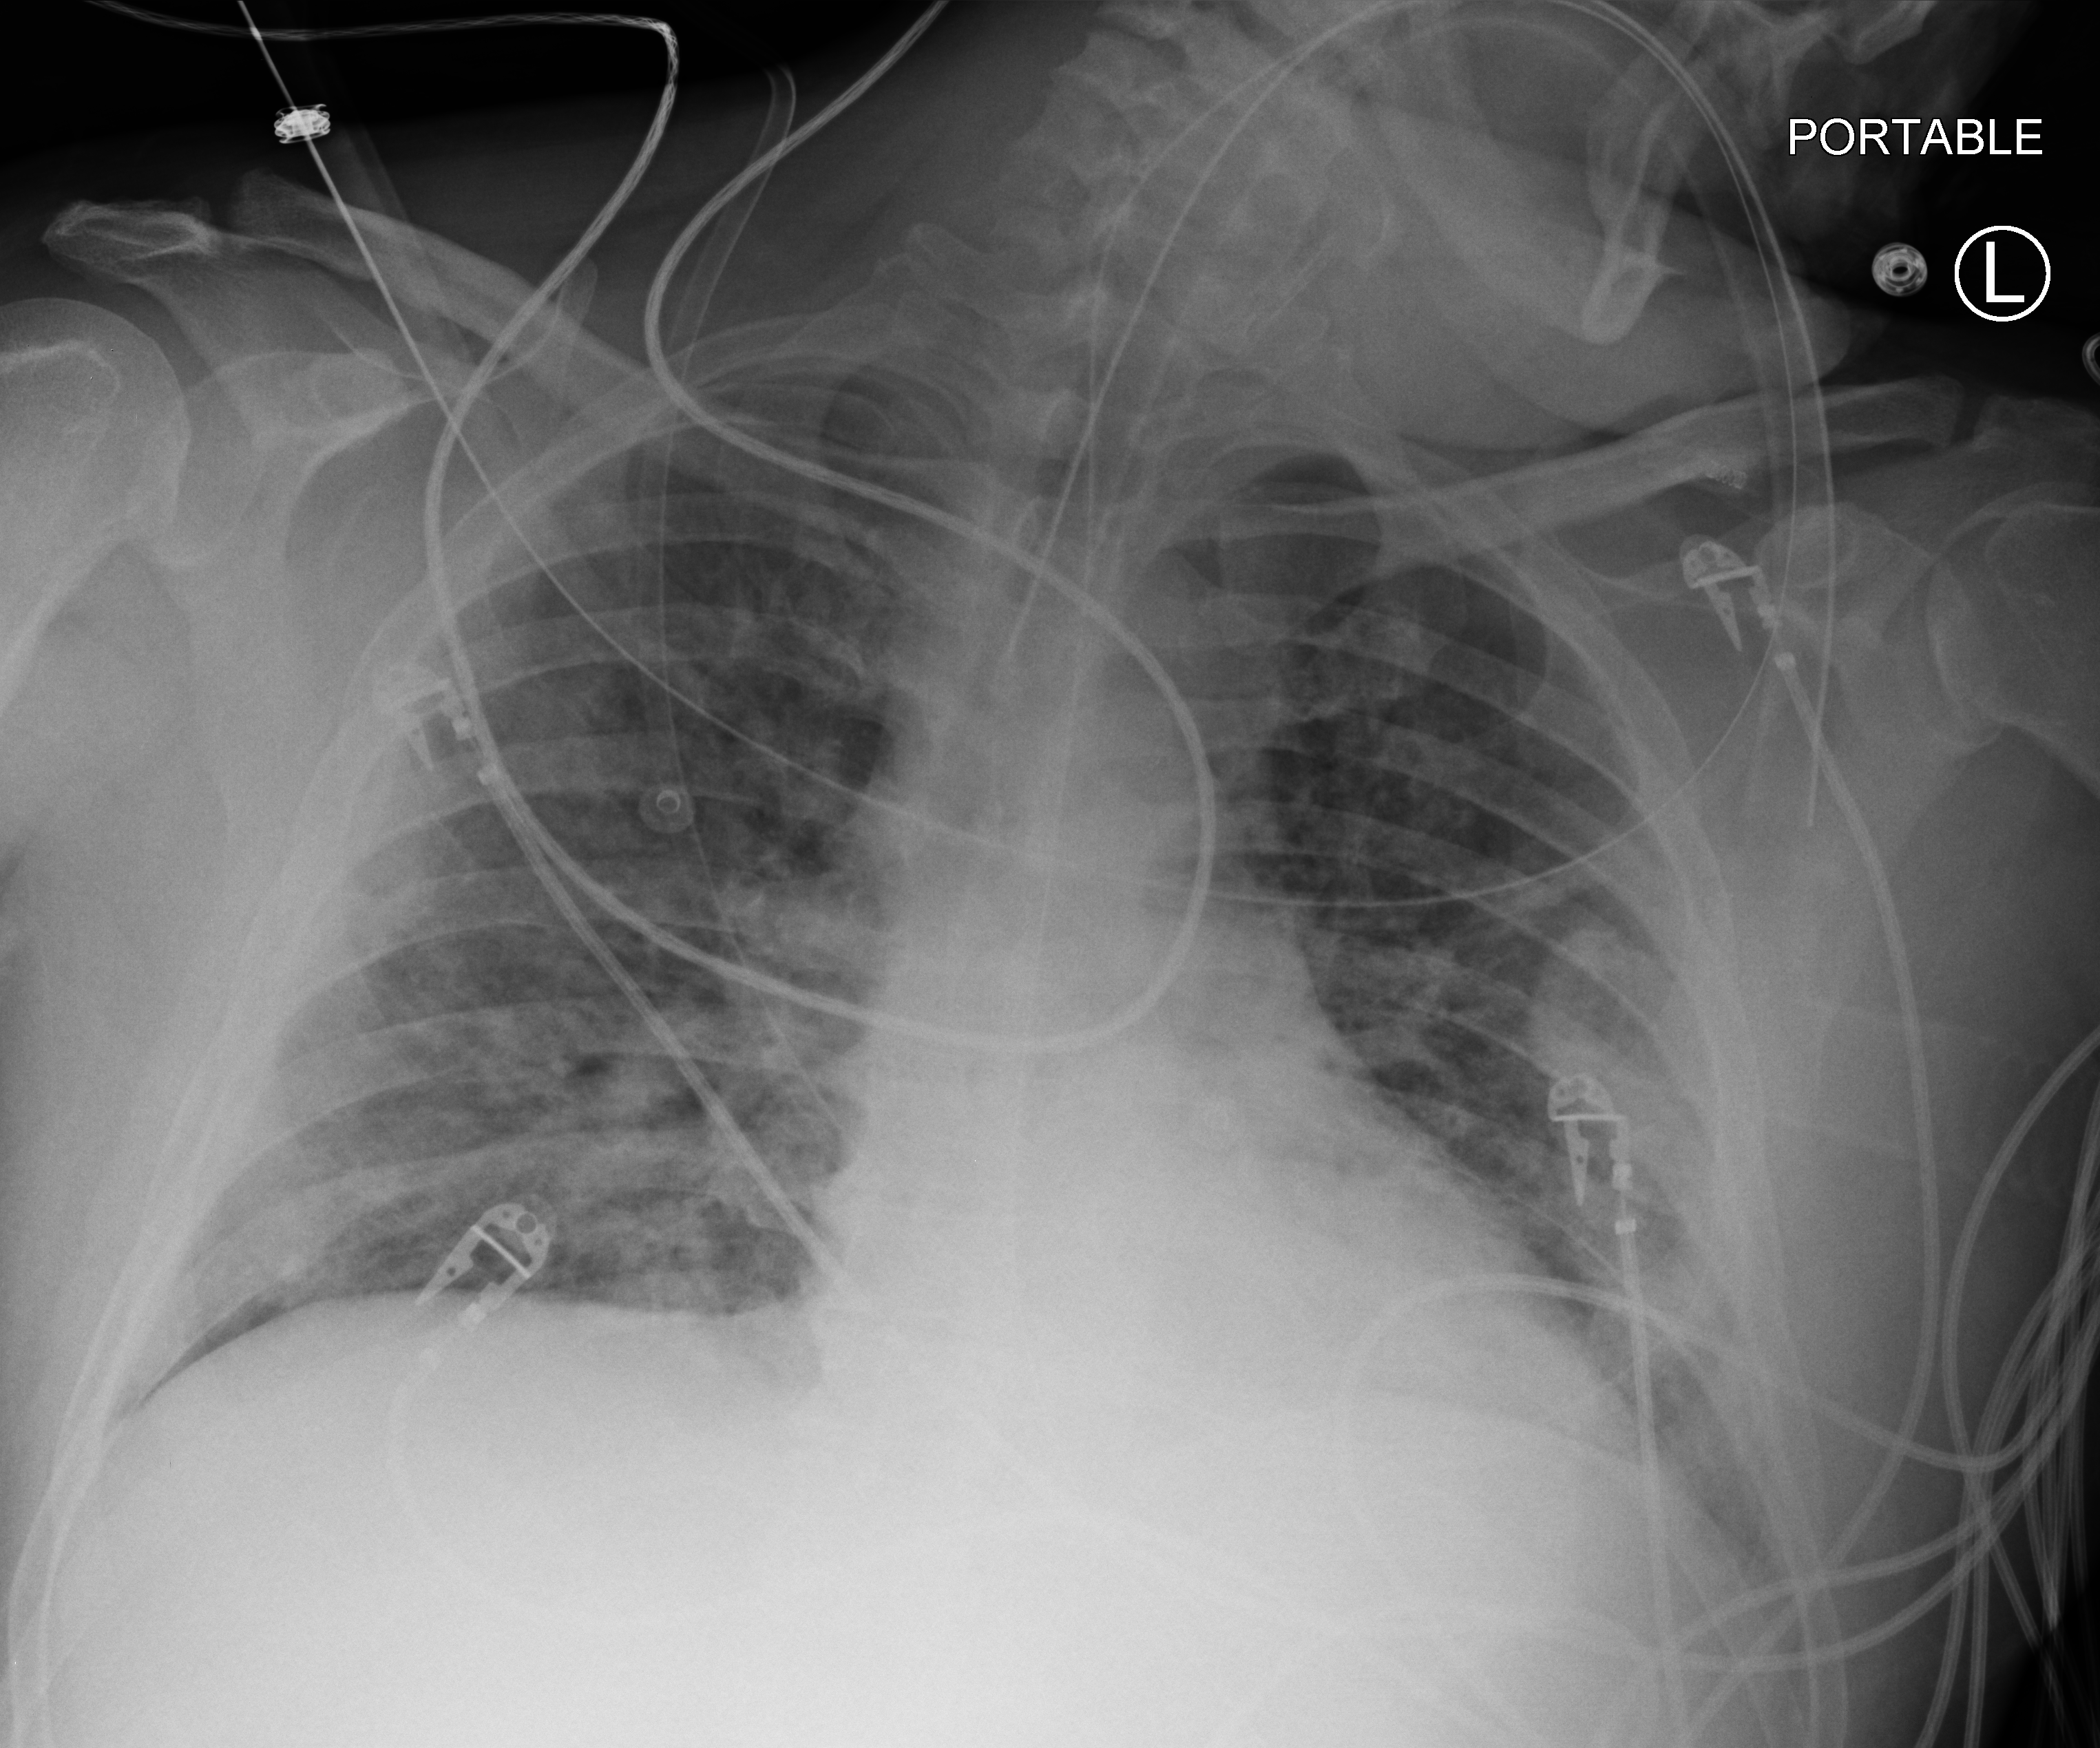
Portable chest radiograph. Patient hospitalised with COVID-19; male, aged 18–59 years.
Hospital-stay facts (about this admission, not read from this image; timing relative to this image not recorded): diabetes (admission record): yes.